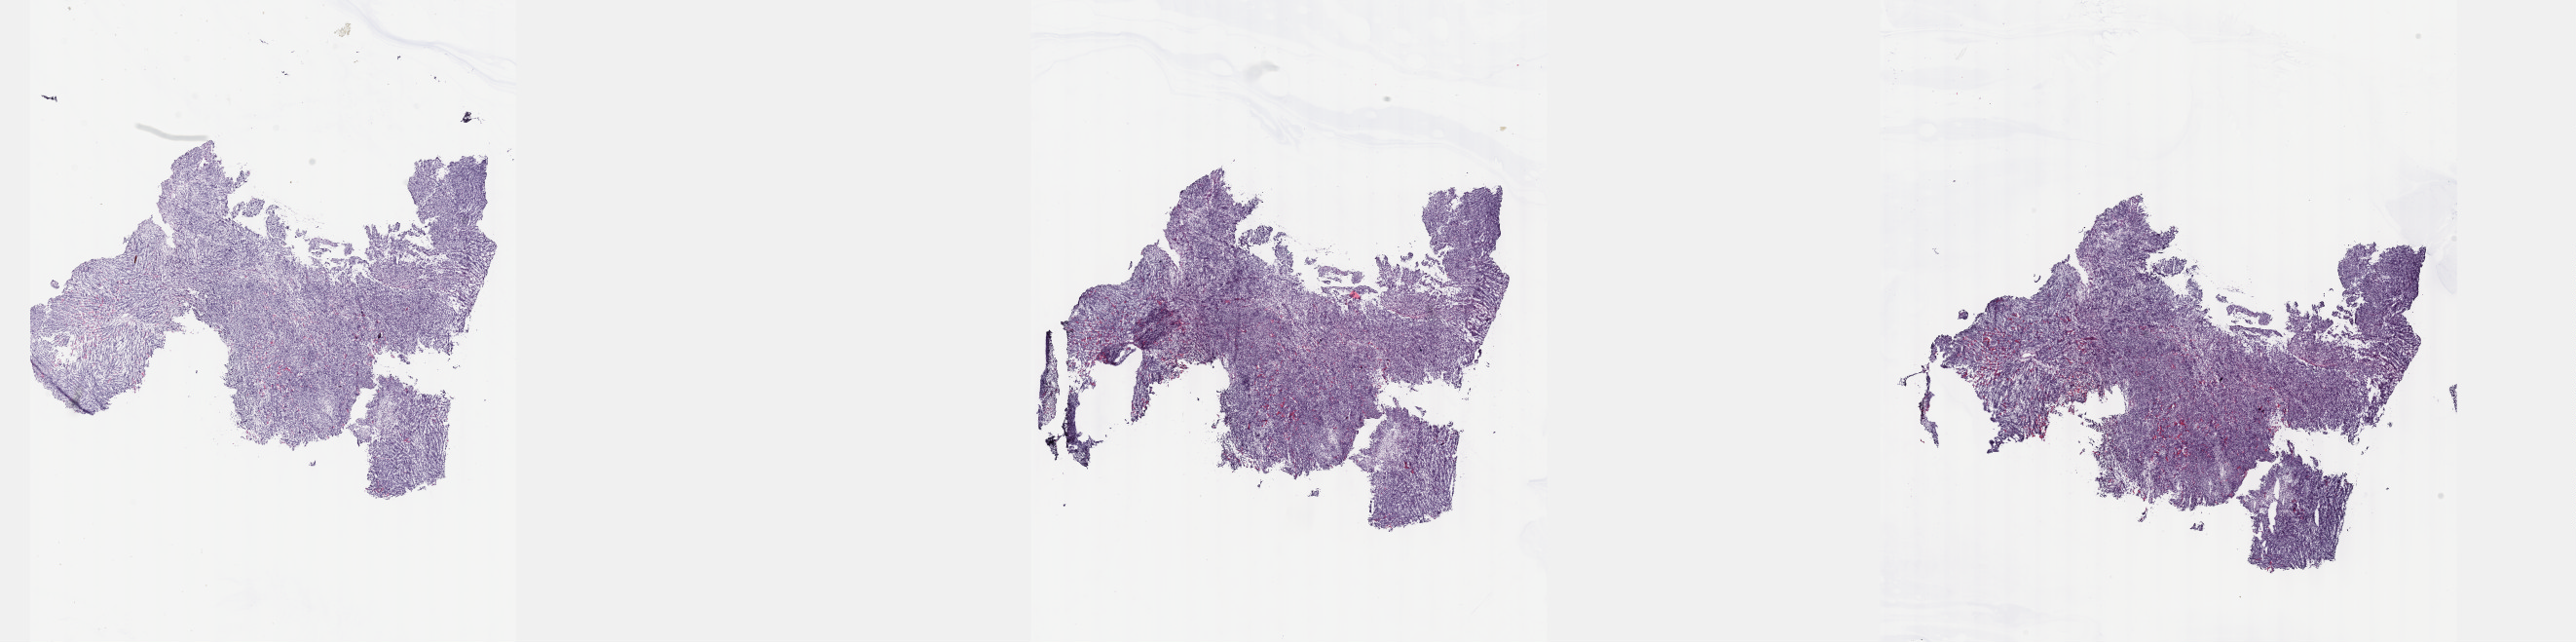
Whole-slide histology image, H&E — low-resolution overview of the scanned area, about 42.8 x 10.7 mm. Frozen section from the top of the tissue portion. Connective, subcutaneous and other soft tissues, primary tumour sample. Patient: female, age at initial diagnosis 24 years. Pathologist review of this section (percent, as recorded): tumour cells 100%, tumour nuclei 80%, normal cells 0%, stromal cells 0%, necrosis 0%. Inflammatory infiltration, as recorded: lymphocyte infiltration 1%, monocyte infiltration 0%, neutrophil infiltration 0%.
* pathologic diagnosis: Synovial sarcoma, biphasic (connective, subcutaneous and other soft tissues of lower limb and hip)